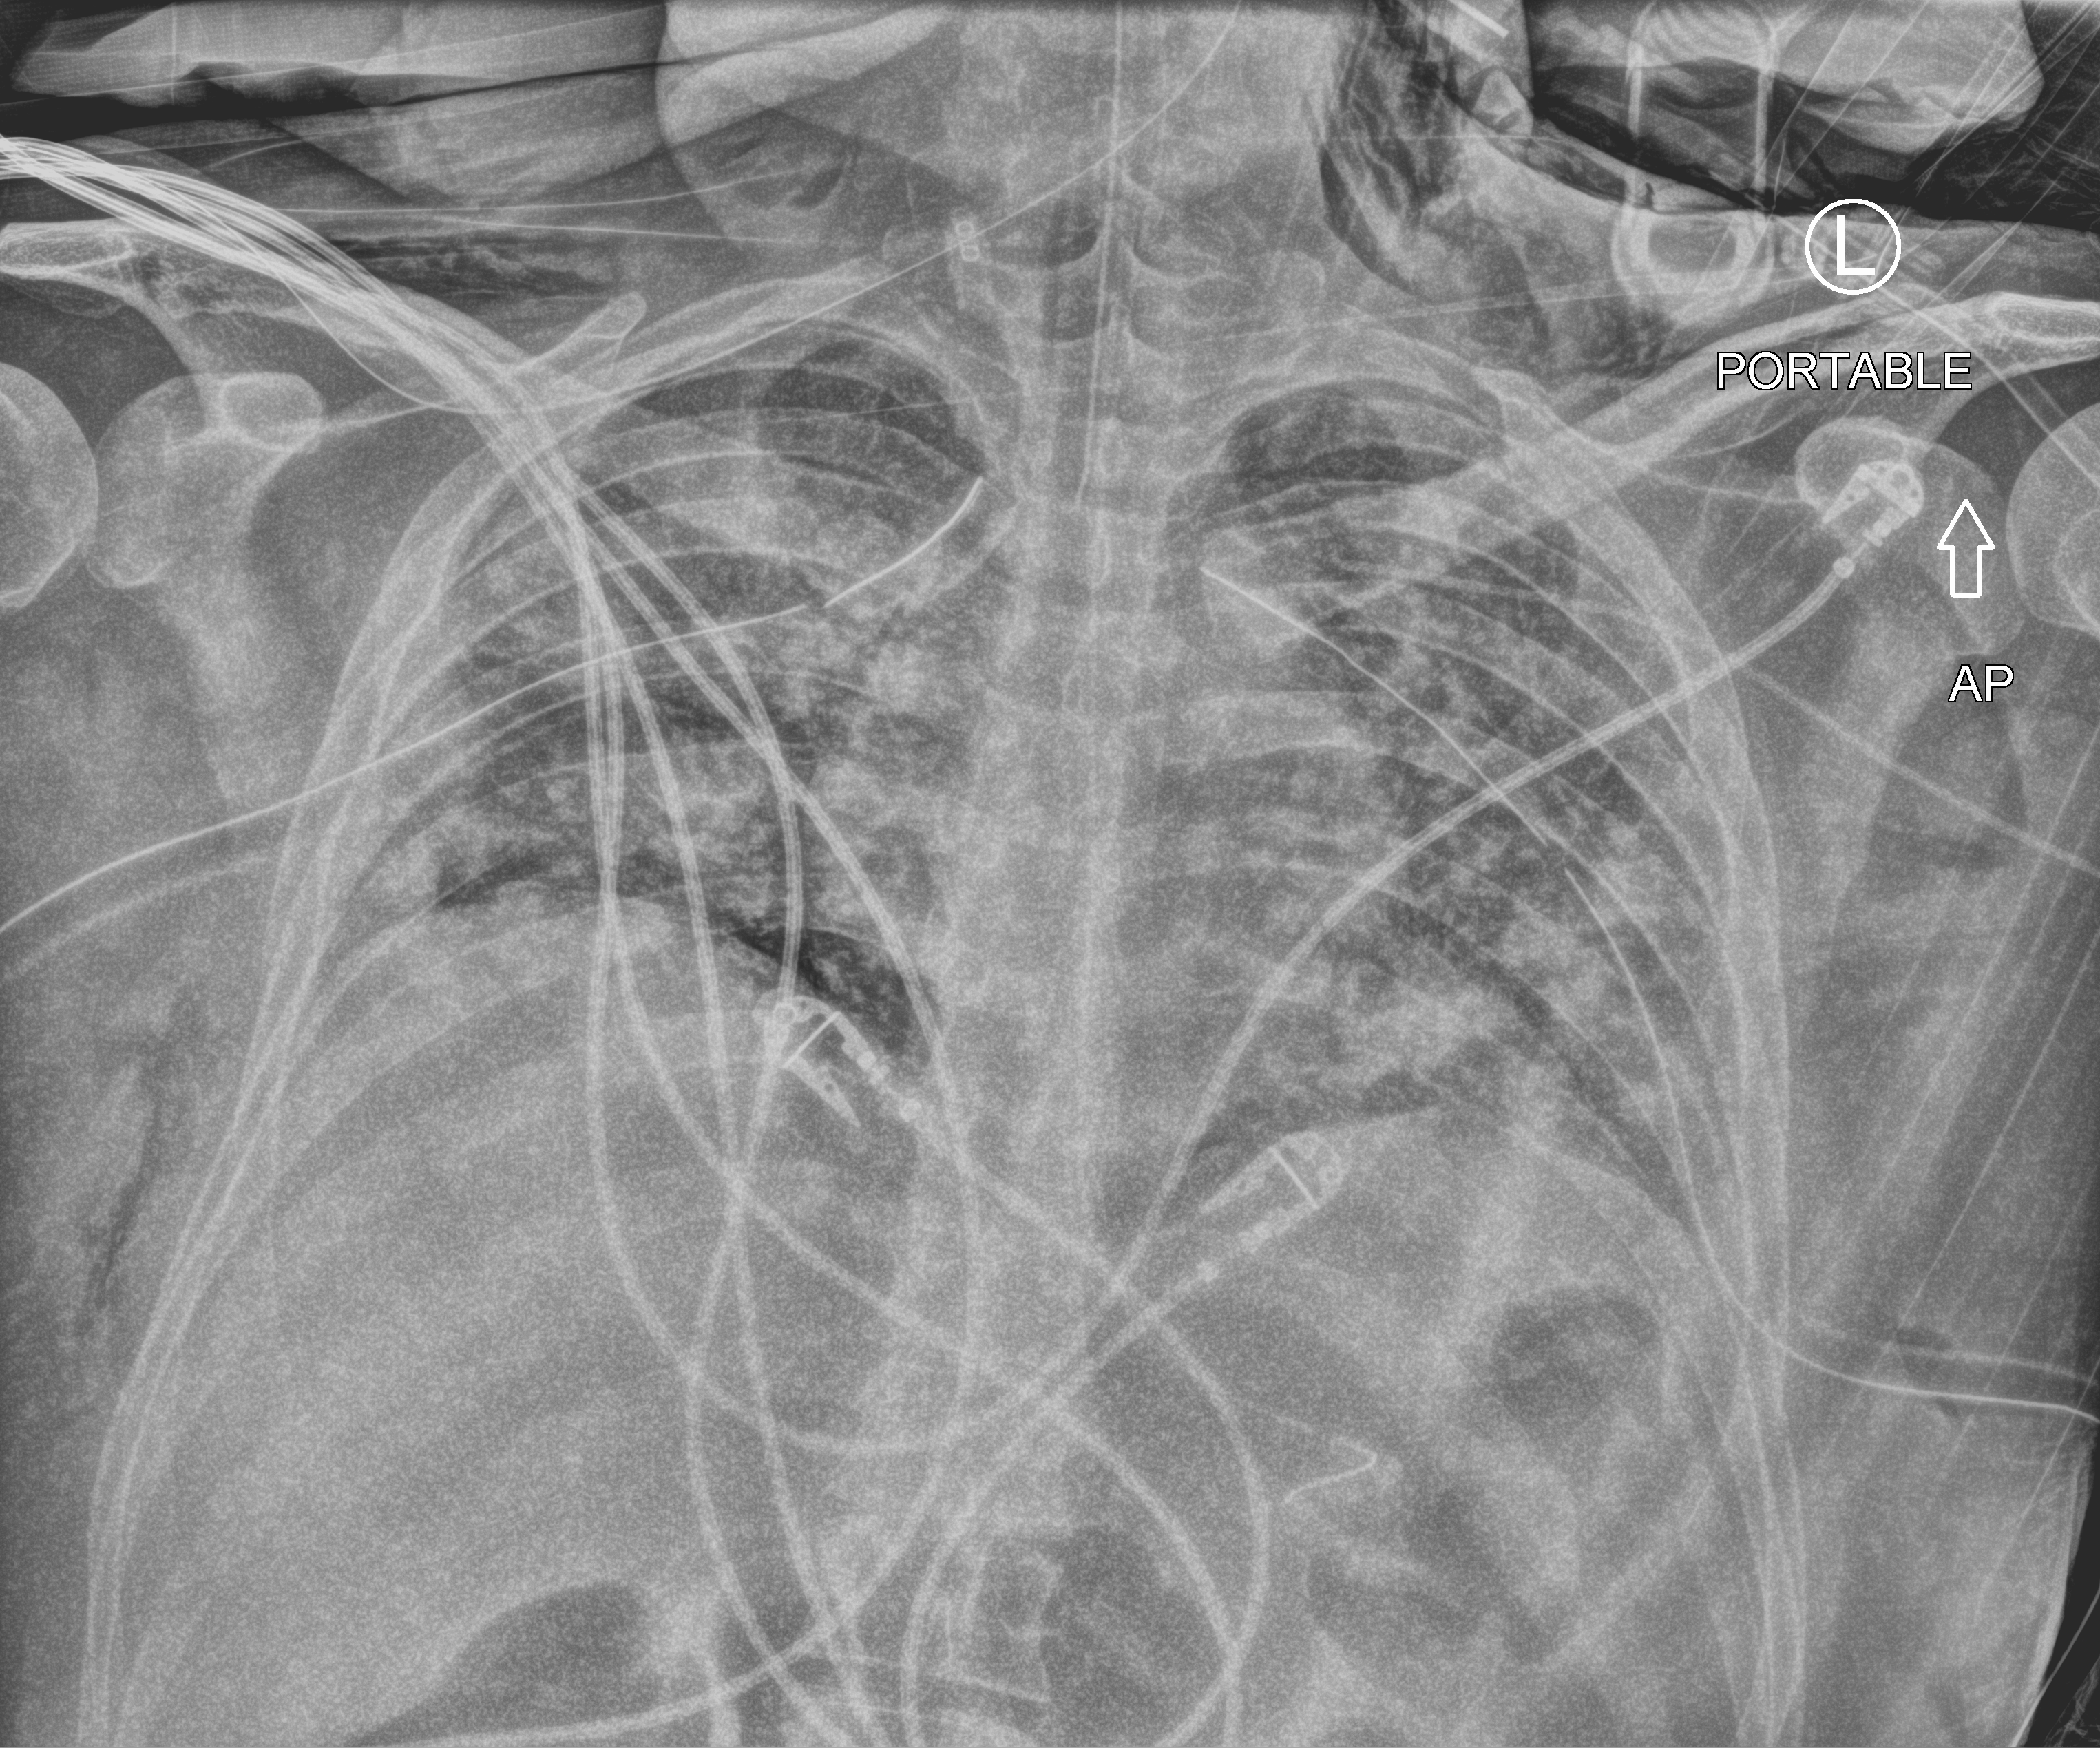
Chest X-ray (portable), anteroposterior (AP) projection. Male patient hospitalised with COVID-19, age 18–59 years.
From the hospital-stay record, not from the radiograph (when in the stay this image was taken is not recorded): mechanically ventilated during this hospital stay: yes; length of hospital stay: 63 days; admitted to intensive care during this hospital stay: yes.